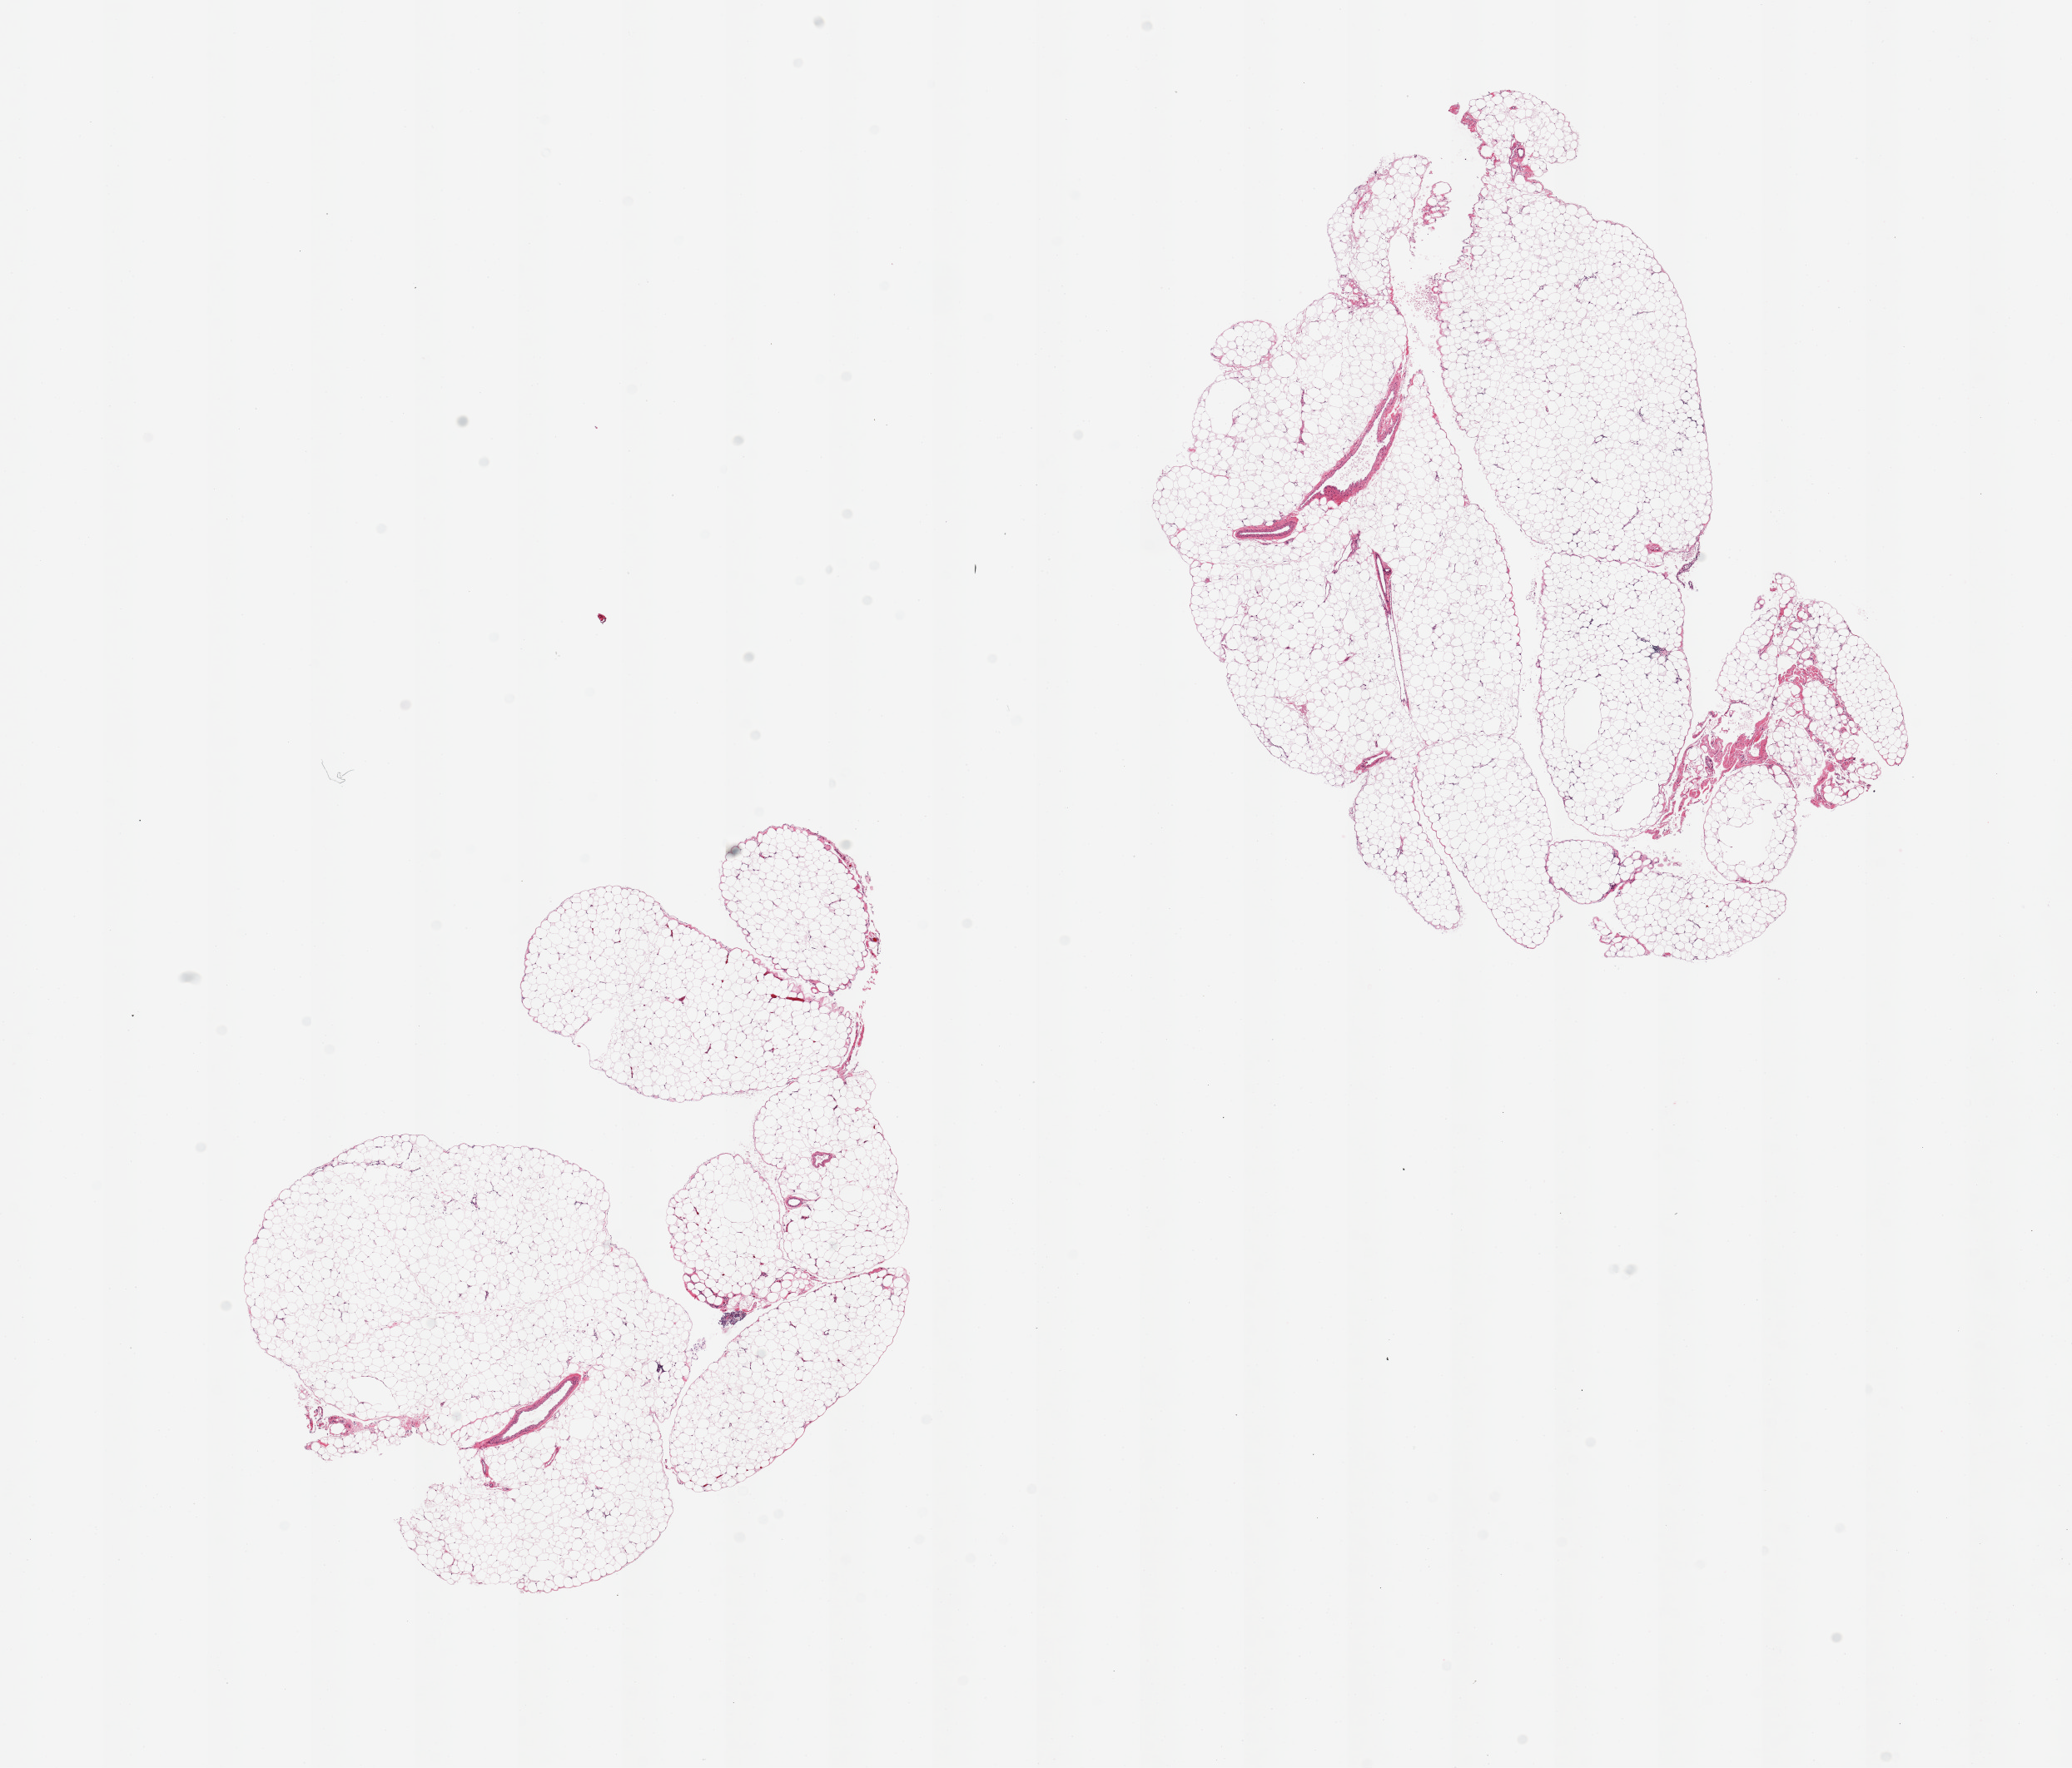
H&E whole-slide image, a low-resolution overview of the entire scanned area, about 19.7 x 16.8 mm (slide scanned at 20x). PAXgene-fixed paraffin-embedded (PFPE) section. Section of omentum (target tissue). Tissue donor sample. Donor: male.
Reviewer comment on this tissue sample: 2 pieces, 7.5x6 & 8x7mm; no artifacts.